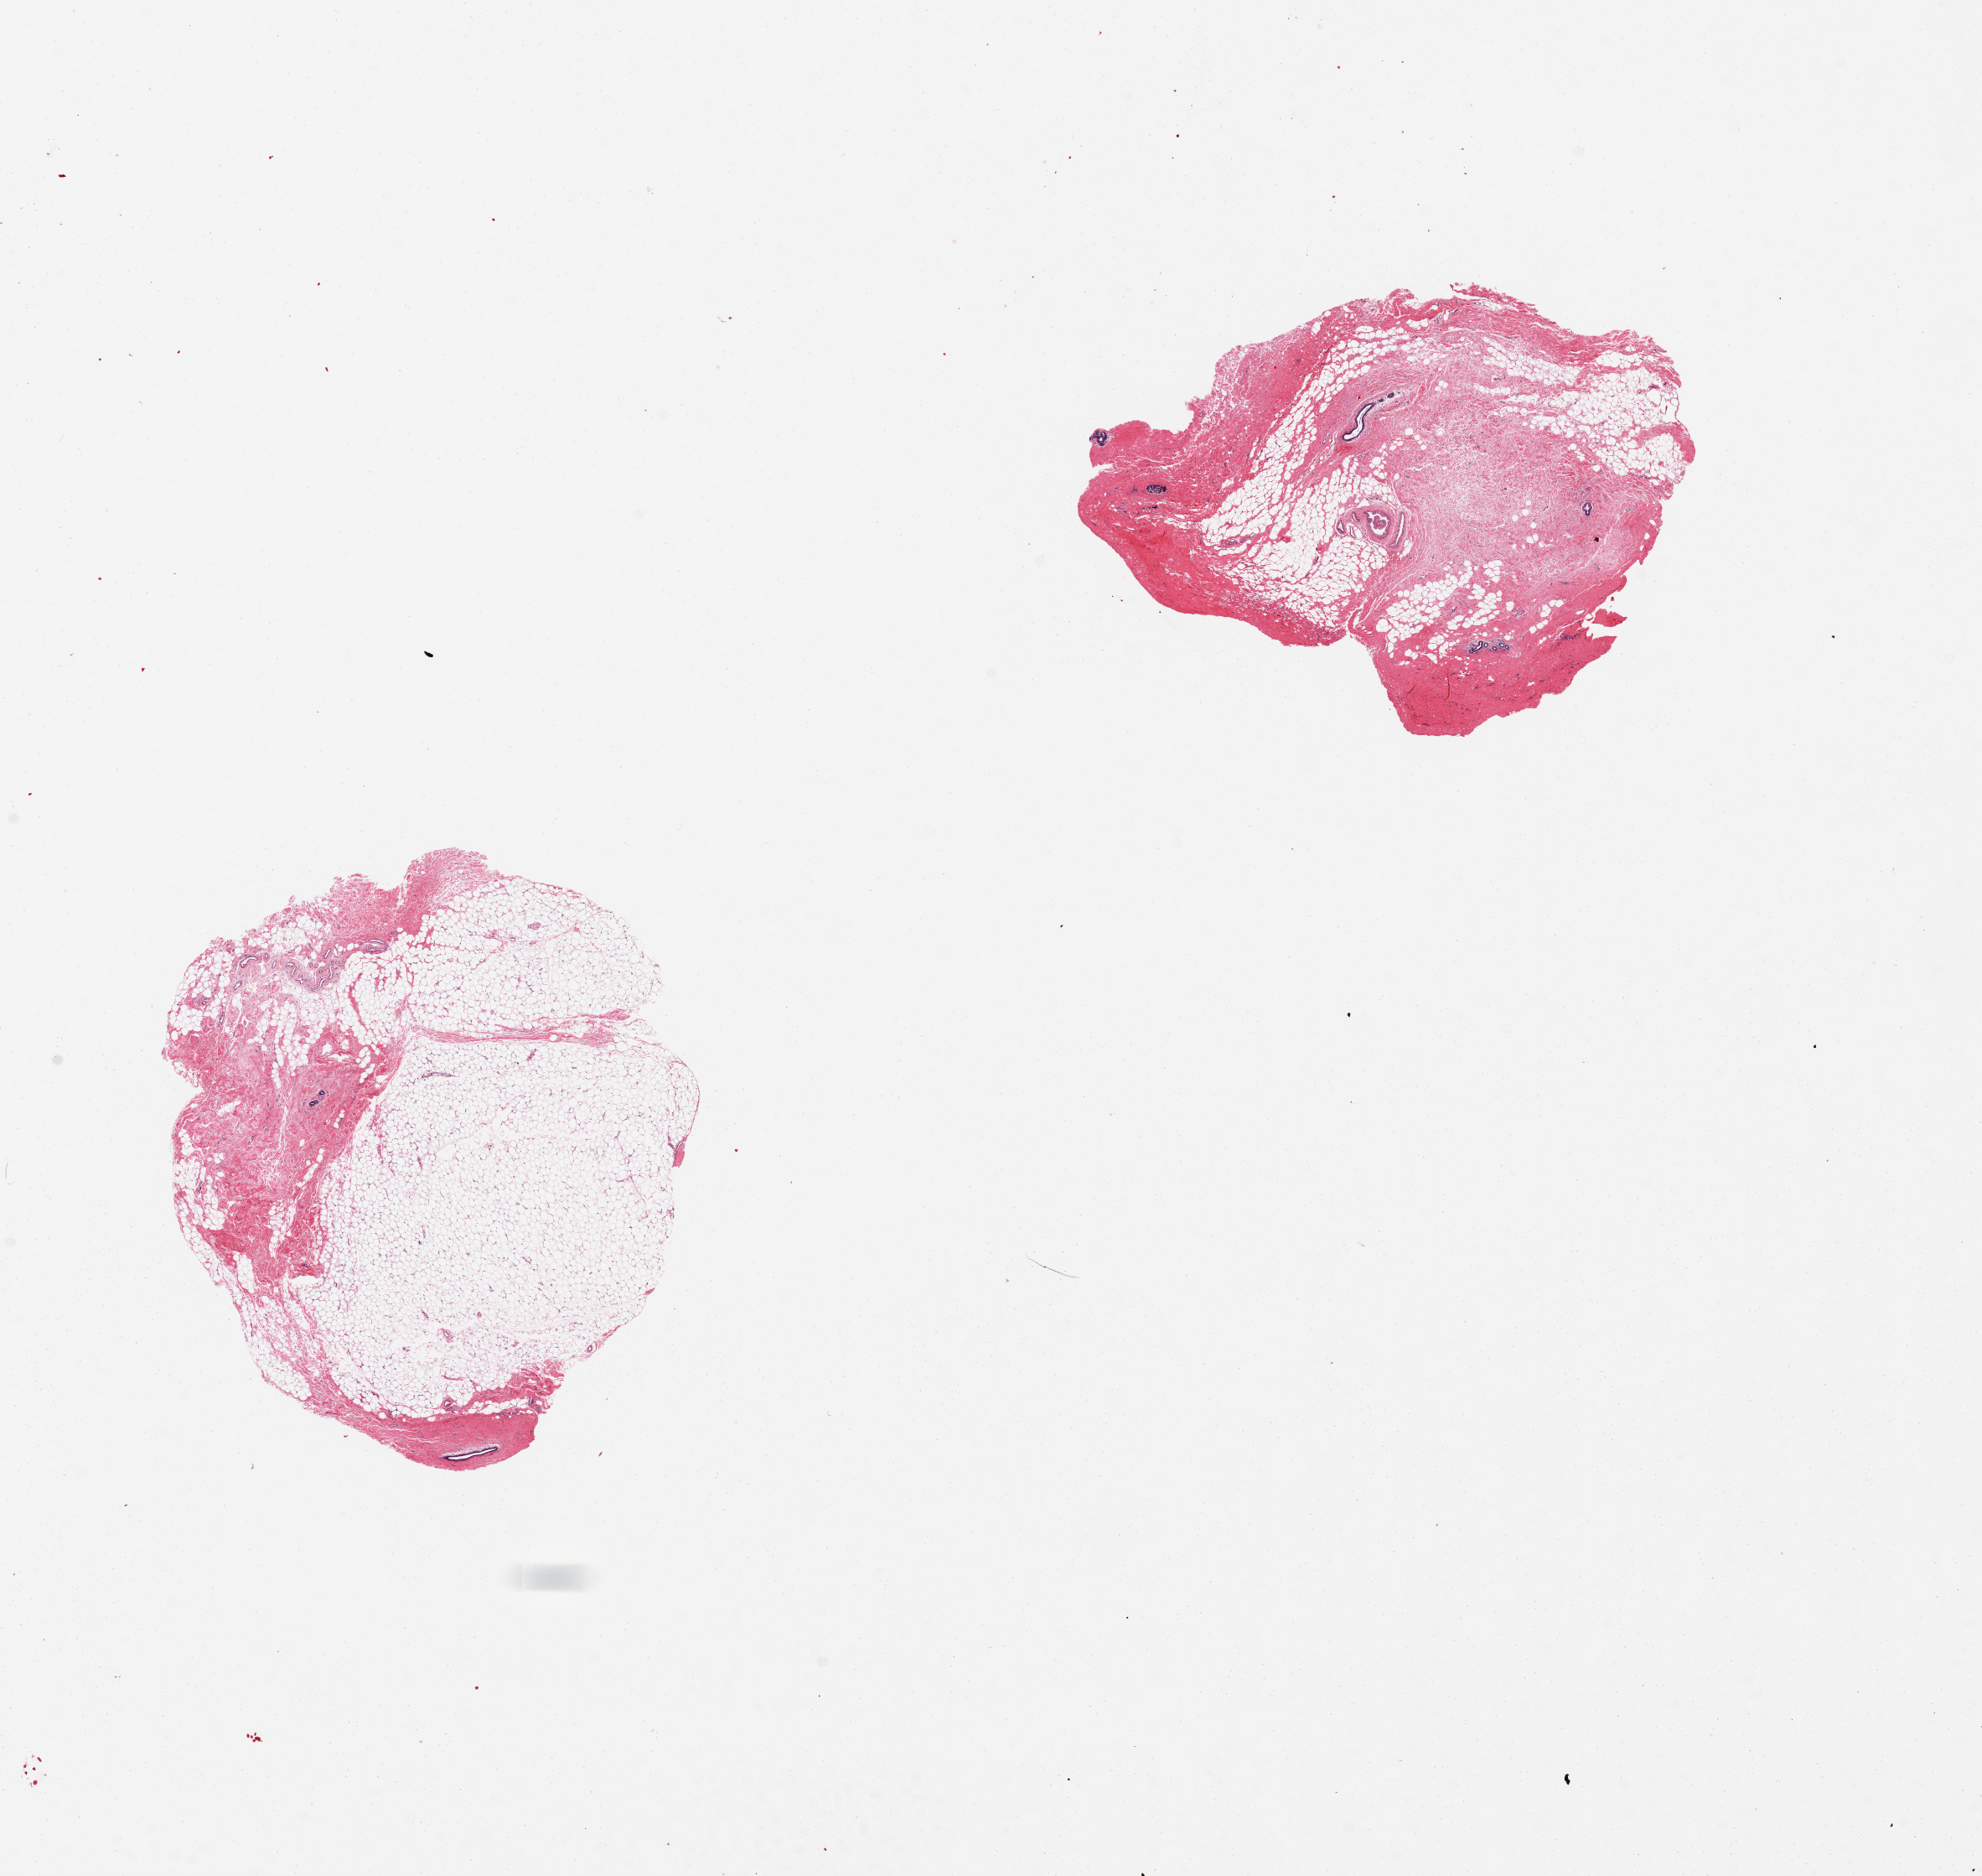
Whole-slide image, hematoxylin and eosin (H&E) stain, shown as a low-resolution overview of the whole scanned area (about 18.7 x 17.7 mm, acquisition: 20x scan), PAXgene-fixed, paraffin-embedded tissue, target tissue: breast, tissue donor sample. Female donor.
- pathologist's review note for this sample: 2 pieces, one is predominantly fatty, second is mostly fibrous stroma, both with few ductal/lobular elements